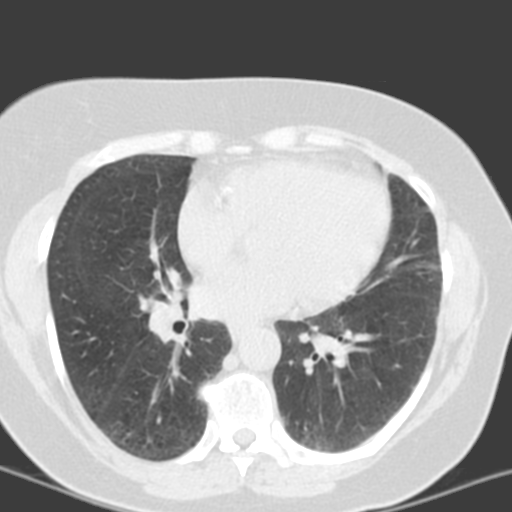
Chest CT (low-dose screening protocol), one axial image. Third annual screen. Lung window (W 1500 / L -600 HU). 3.2 mm slice thickness. Slice 76 of 150 in the series. 512 × 512 image matrix. Female, age 55 years at enrolment. Current smoker at enrolment.
• Expert reader's lesion annotation, bounding box (x1, y1, x2, y2) in pixels: (273, 401, 357, 460).
• The screening reader recorded 6 non-calcified nodules or masses ≥4 mm on this exam; which of them this box marks is not recorded.
• Official screen result: positive, no significant change: stable abnormalities potentially related to lung cancer, unchanged since the prior screening exam.